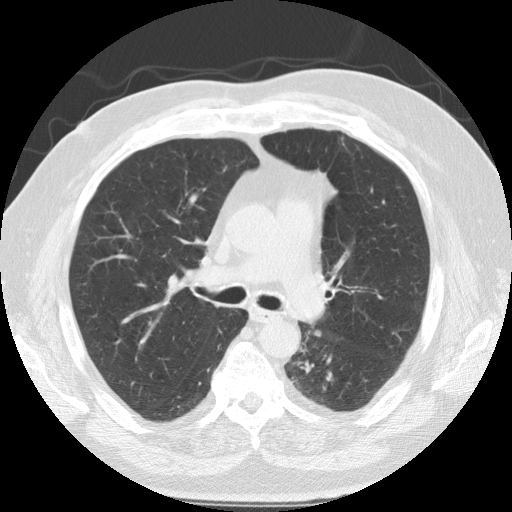
Low-dose screening chest CT, one axial slice. Position 75 of 124 along the scan axis. Reconstruction kernel STANDARD. 120 kVp. Lung window (W 1500 / L -600 HU). 2.5 mm slice thickness. 512 × 512 image matrix, field of view 360 × 360 mm.
Outlined on this slice (outlined manually by an expert reader):
- lesion 1 (tumor, lower lobe of left lung): bounding box <300,361,314,373> (left, top, right, bottom; pixels)